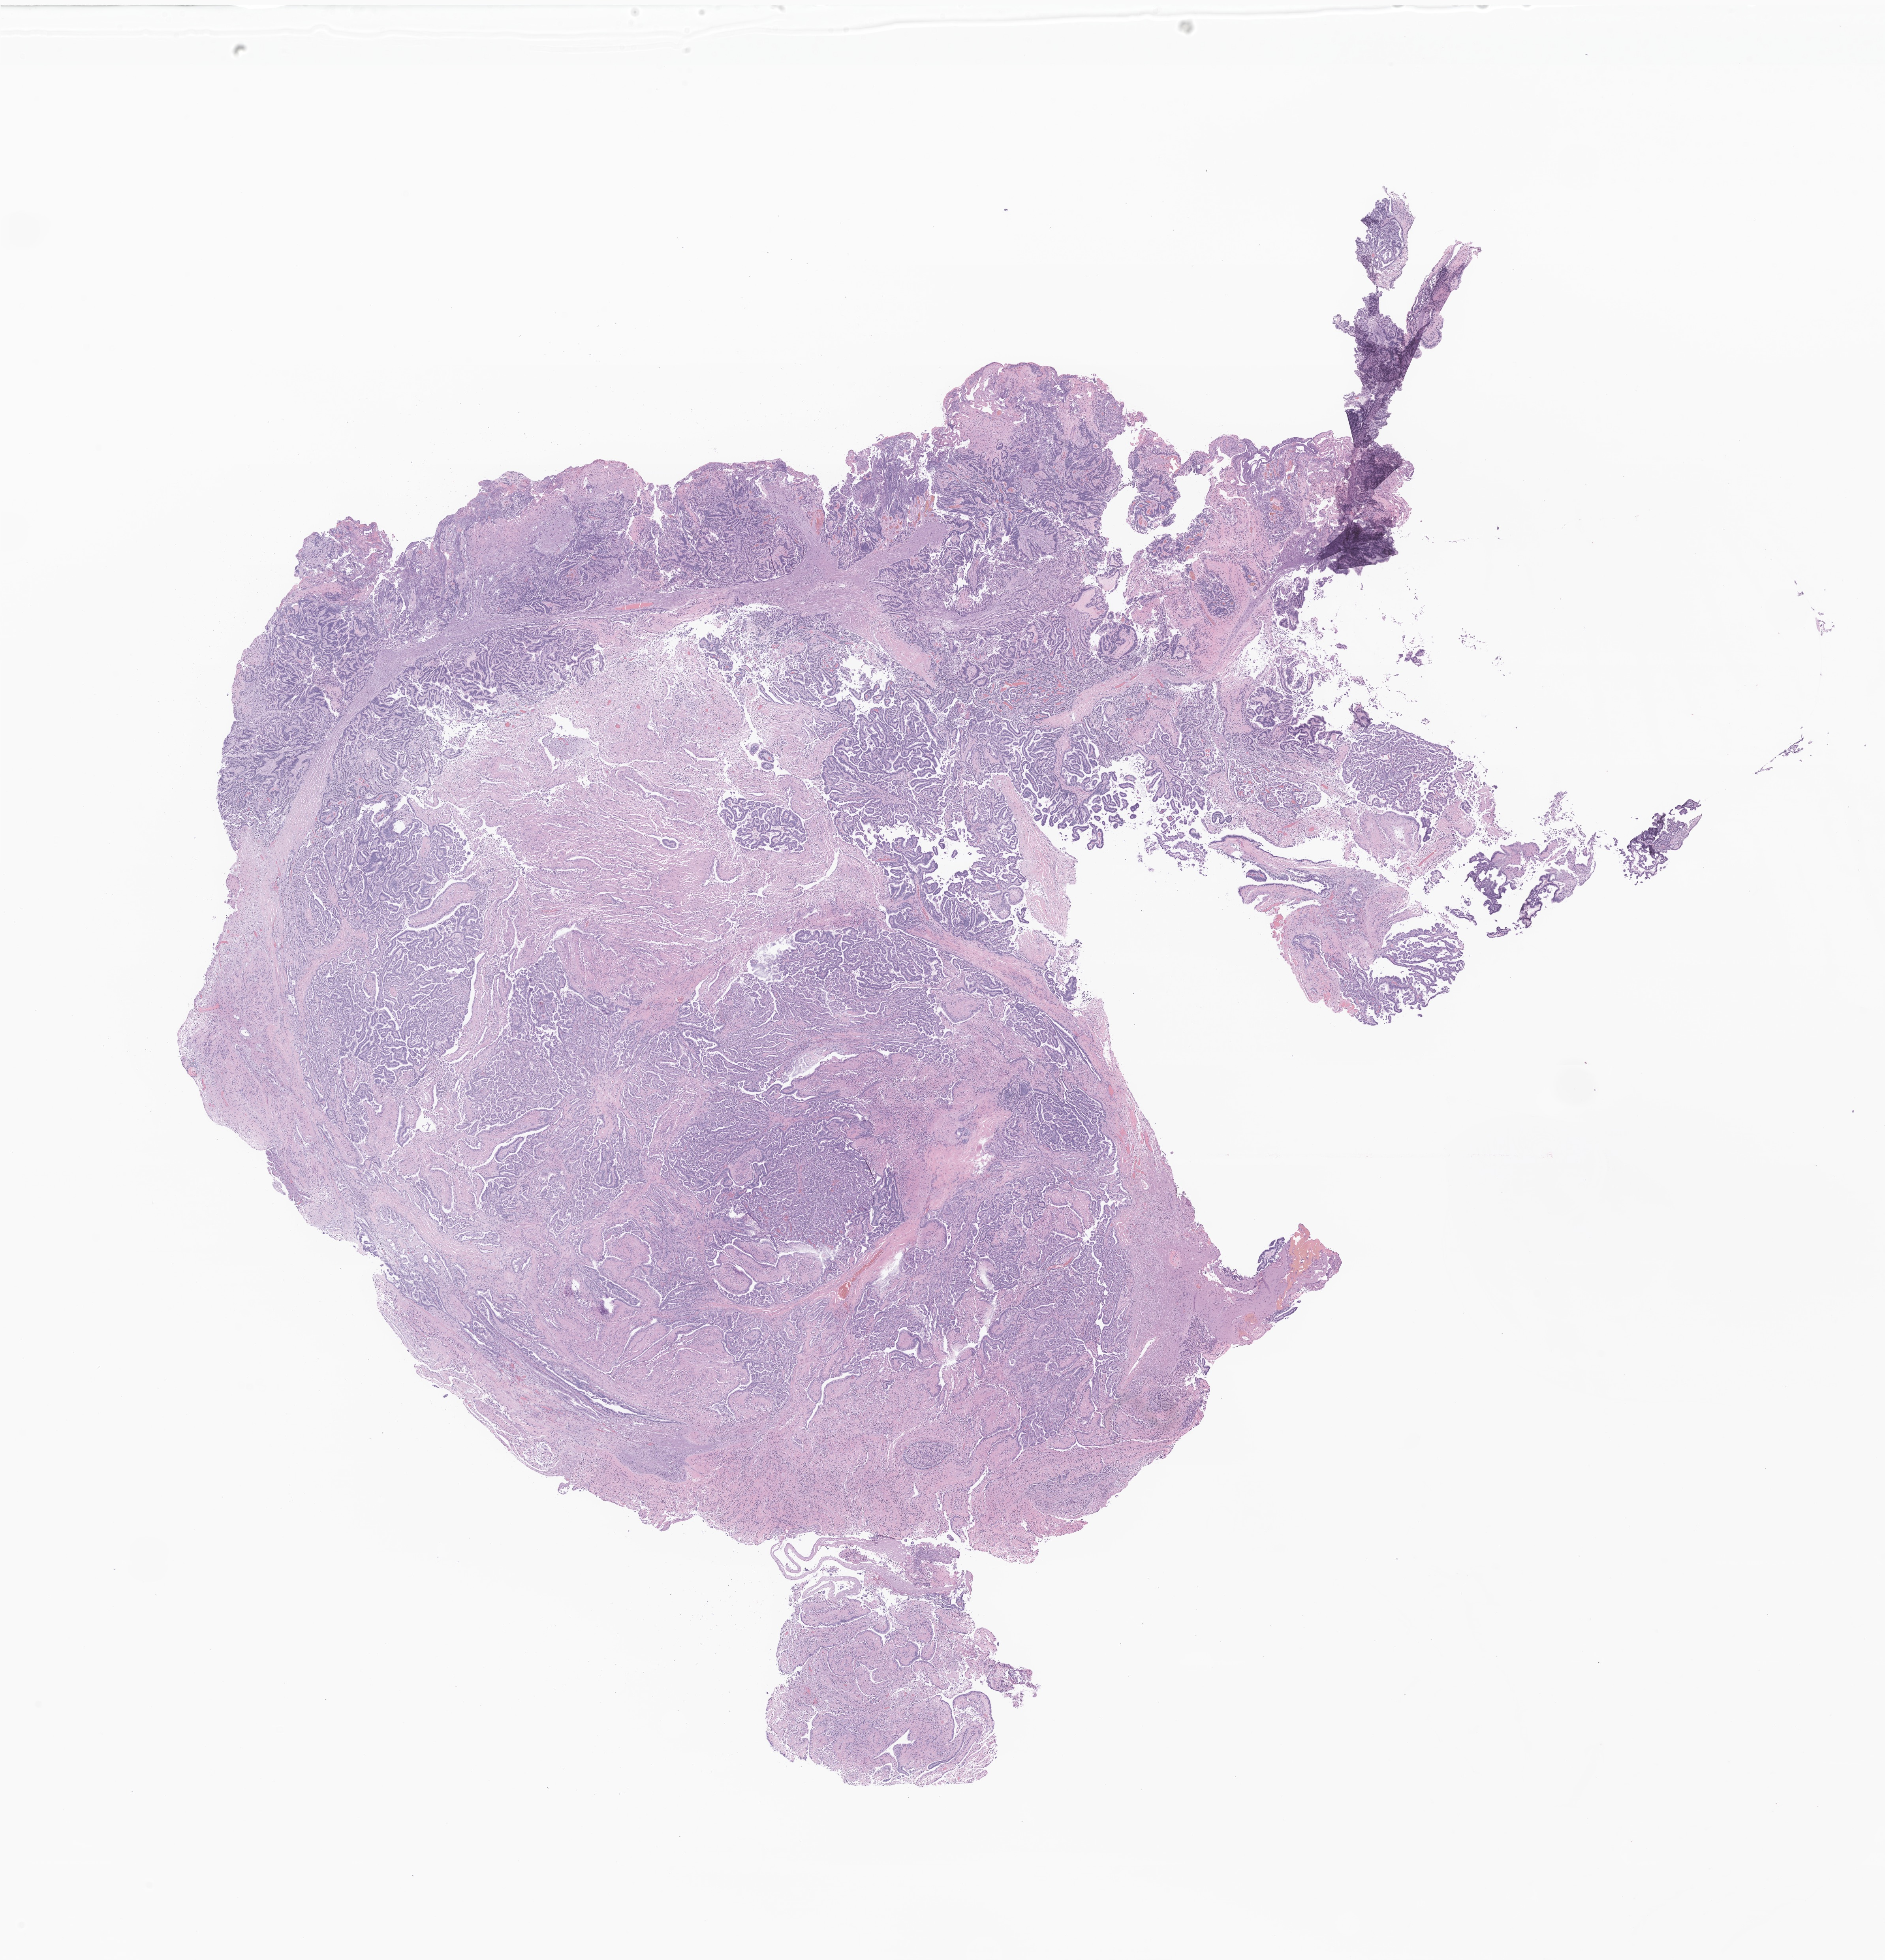
H&E whole-slide image of tumor tissue from the temporal lobe — shown as a low-resolution overview of the whole scanned area (about 20.1 x 20.9 mm). FFPE section. Male patient, age 344 days.
• diagnosis (ICD-O-3 morphology term): Atypical choroid plexus papilloma